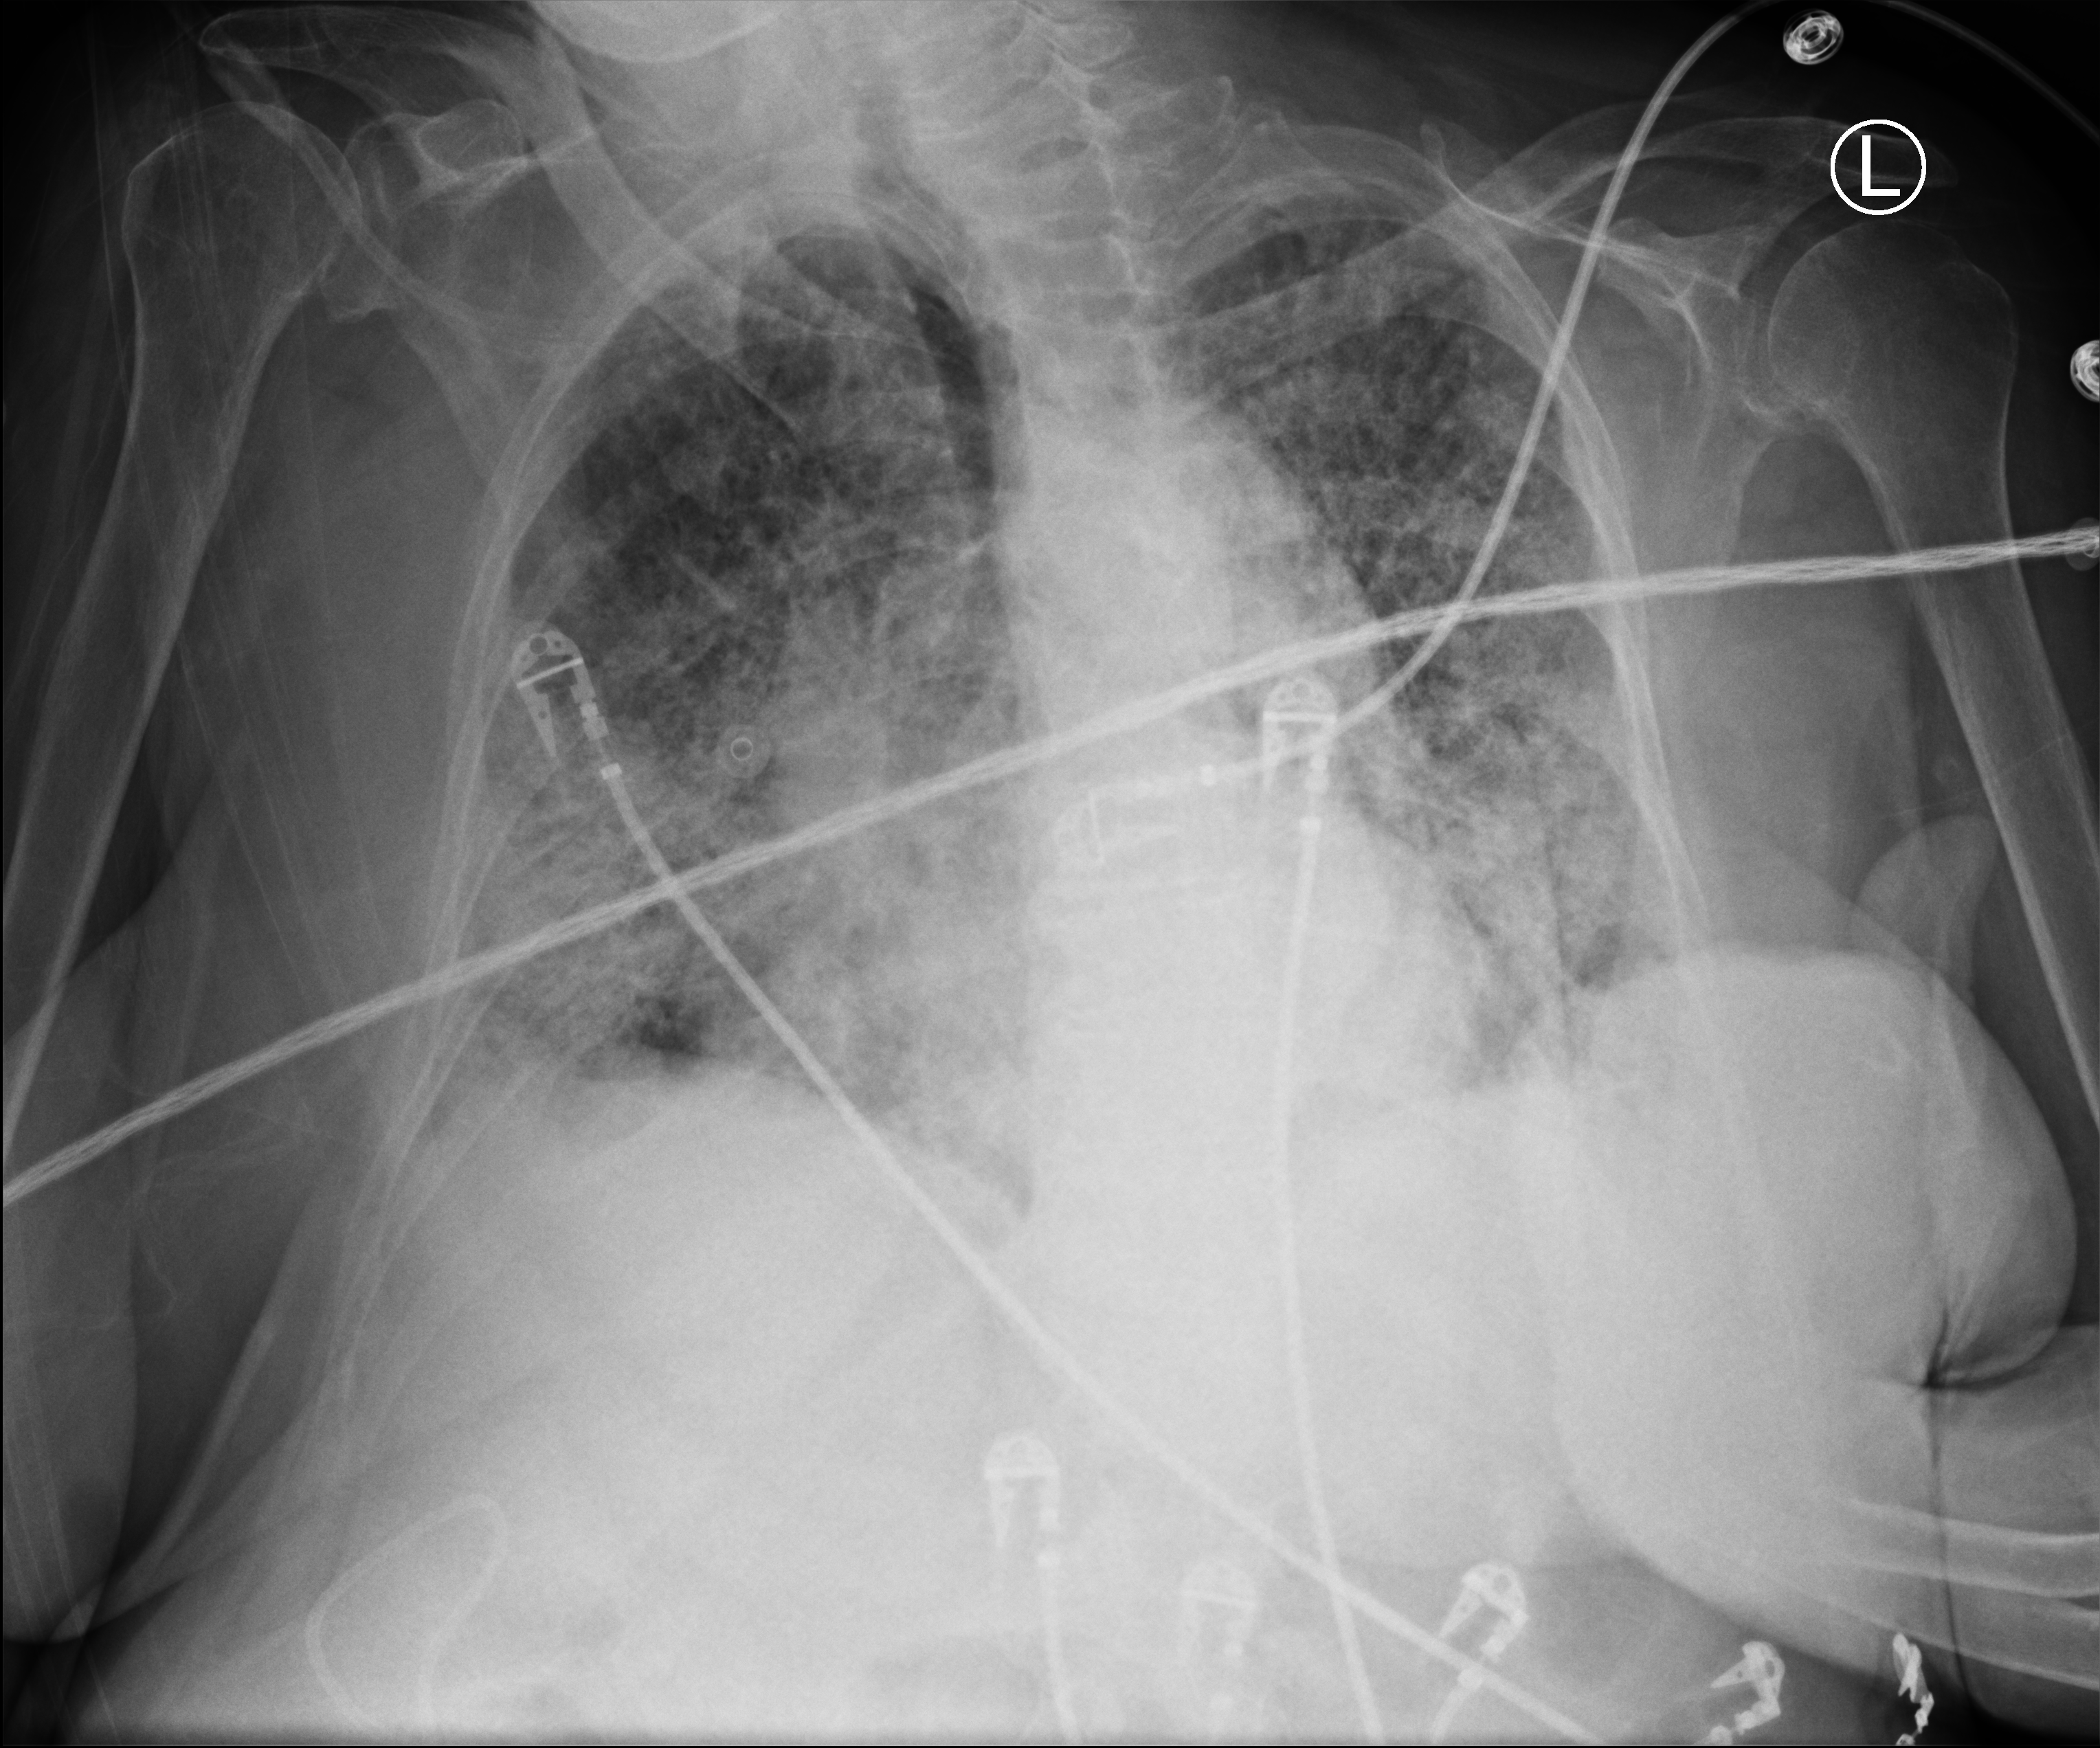
Chest X-ray (portable), anteroposterior (AP) projection. Female patient hospitalised with COVID-19, age 75–90 years.
From the hospital-stay record, not from the radiograph (when in the stay this image was taken is not recorded):
- diabetes (admission record): yes